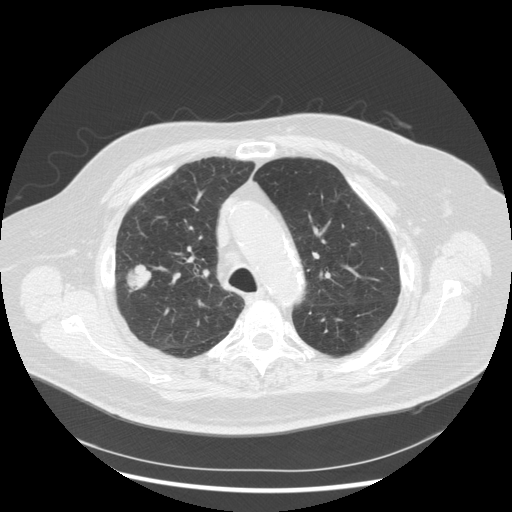
Chest CT (low-dose screening protocol), one axial image; third screening round (two years after baseline); lung window (W 1500 / L -600 HU); 2.5 mm slice thickness; slice 204 of 263 in the series. Male, age 72 years at enrolment. Former smoker at enrolment.
Lesion marked by an expert reader, box from (x=111, y=252) to (x=164, y=302) px. Reader record for this screening exam (exam-level; its link to the box is not recorded): non-calcified nodule or mass ≥4 mm, right upper lobe, 31 × 31 mm, poorly defined margins, soft tissue attenuation, pre-existing on the prior screen: no. Official screen result: positive, other. Lung cancer was diagnosed 70 days after this screen: squamous cell carcinoma, NOS, right upper lobe, poorly differentiated (G3), stage IIIA (AJCC 6th edition), 19 mm at pathology.